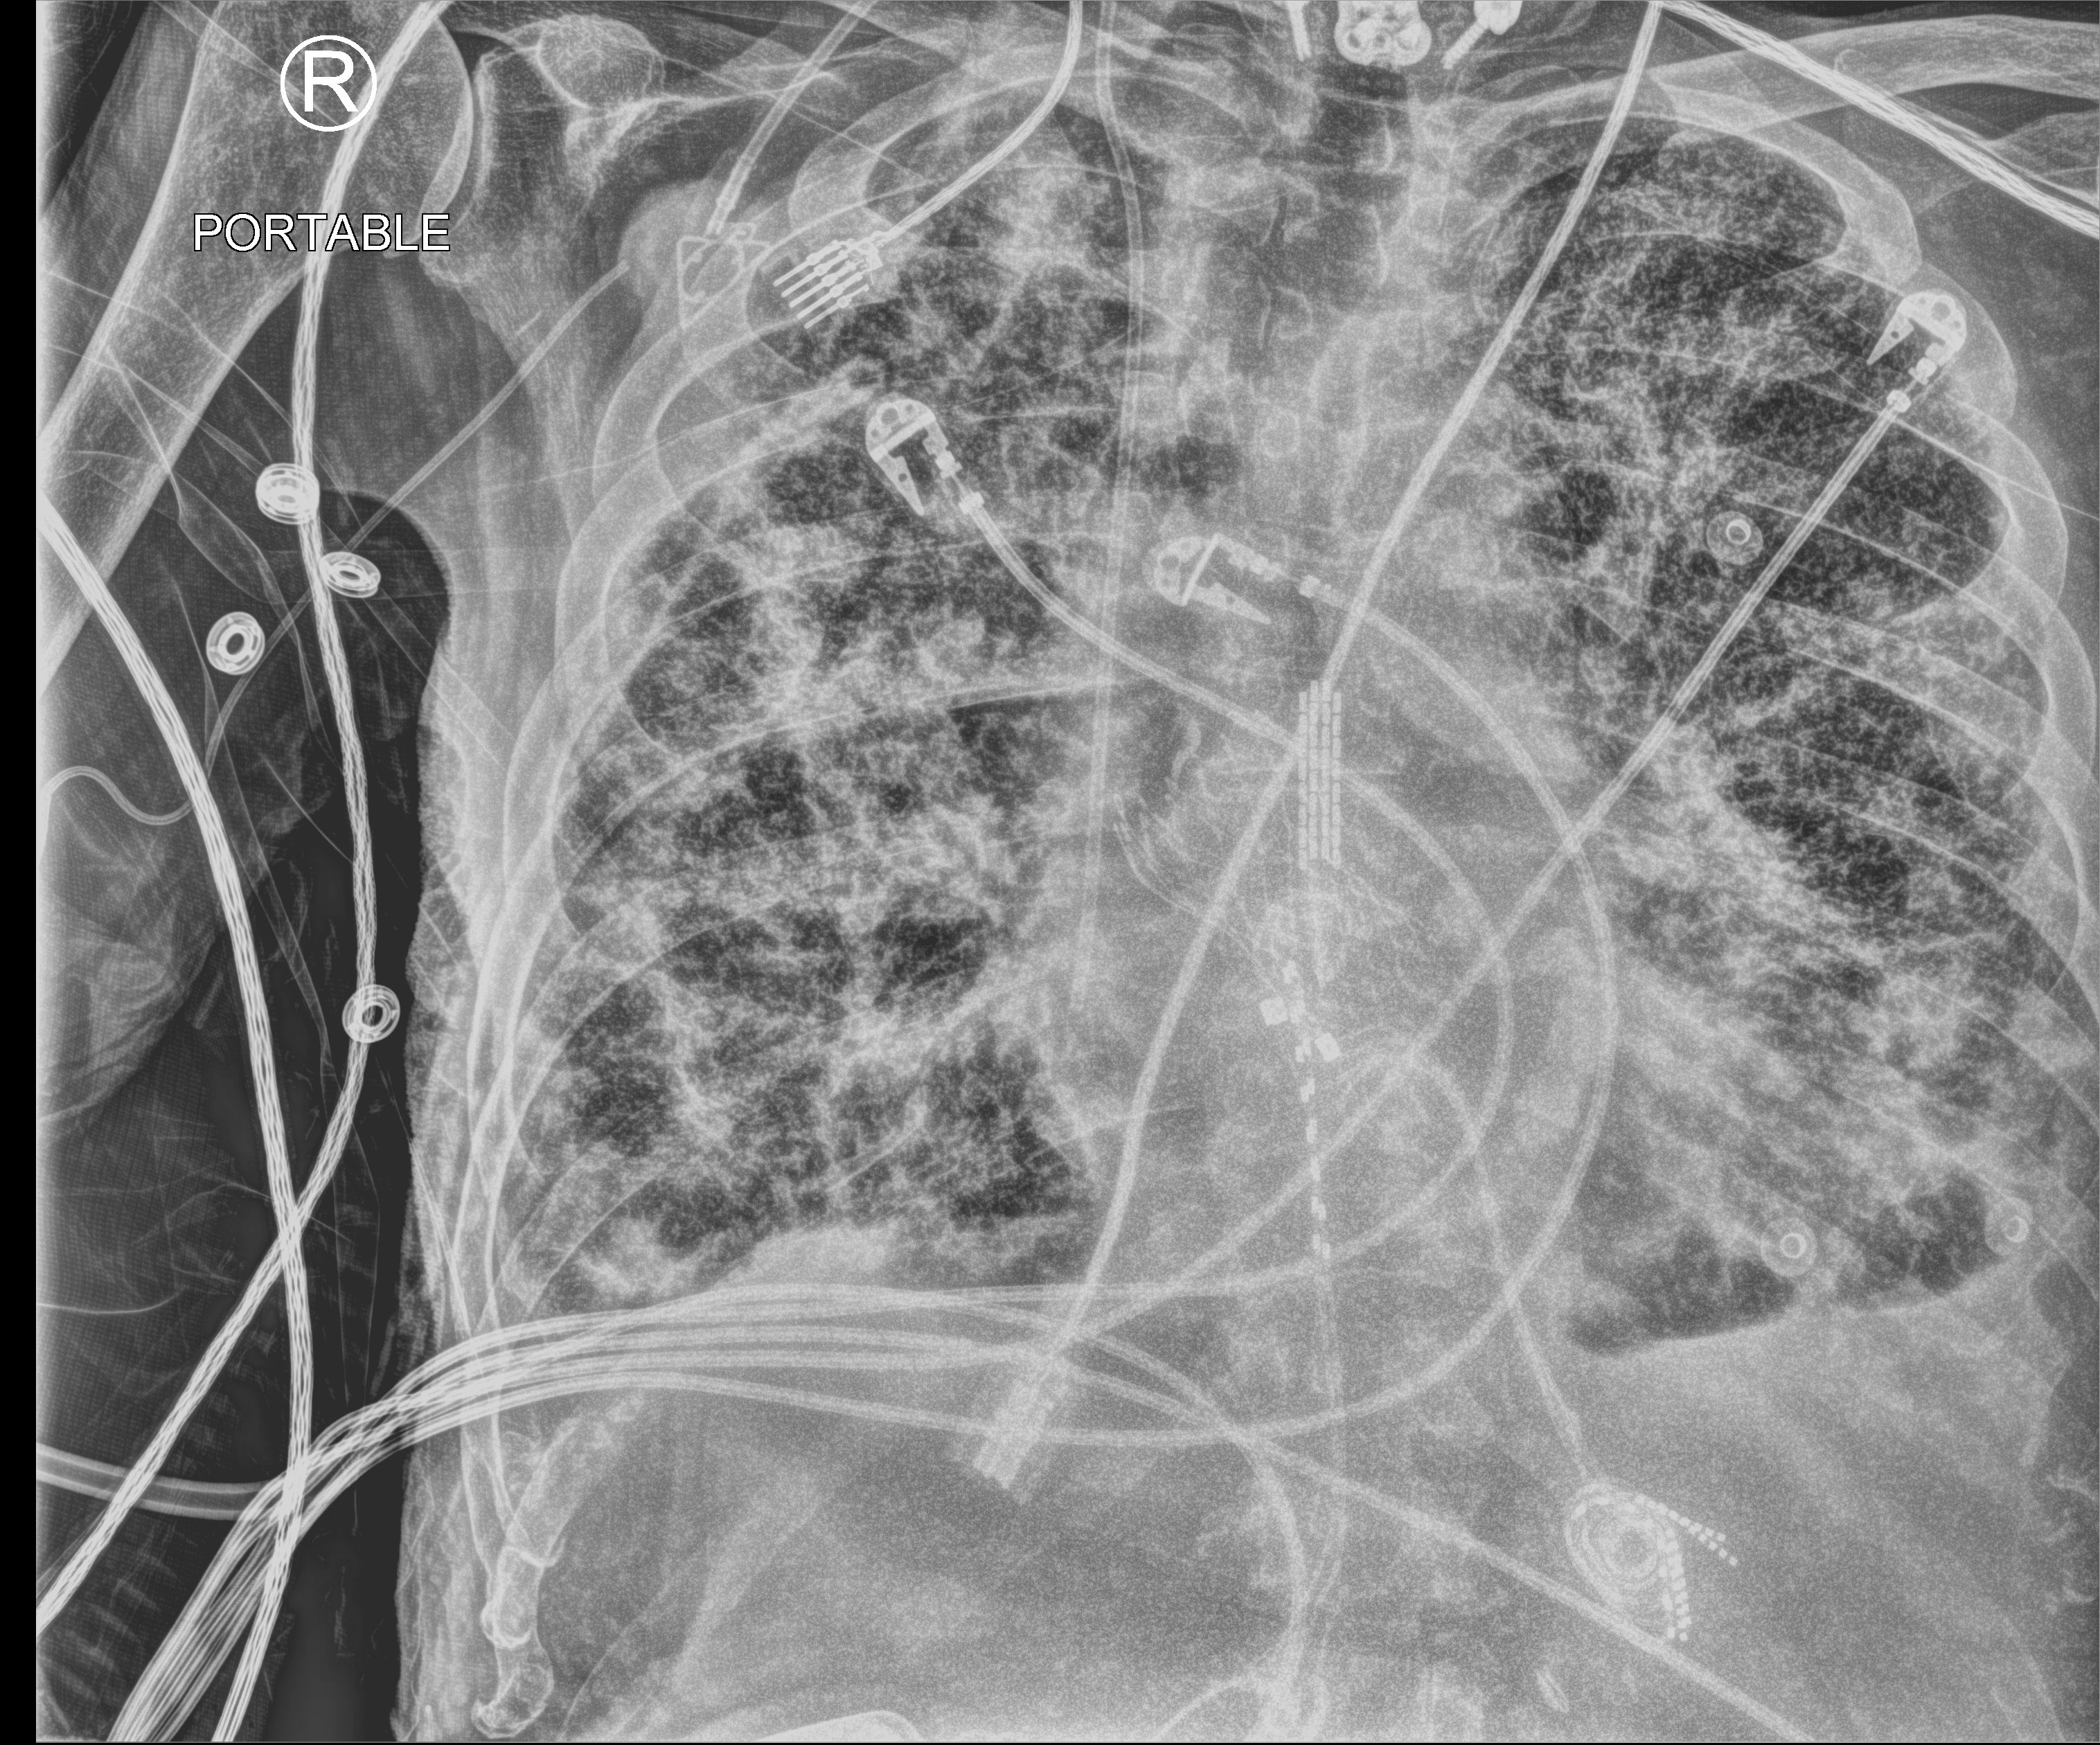
Chest X-ray (portable), anteroposterior (AP) projection. Male patient hospitalised with COVID-19, age 75–90 years.
From the hospital-stay record, not from the radiograph (when in the stay this image was taken is not recorded):
- smoking status (admission record): former
- mechanically ventilated during this hospital stay: no
- admitted to intensive care during this hospital stay: yes